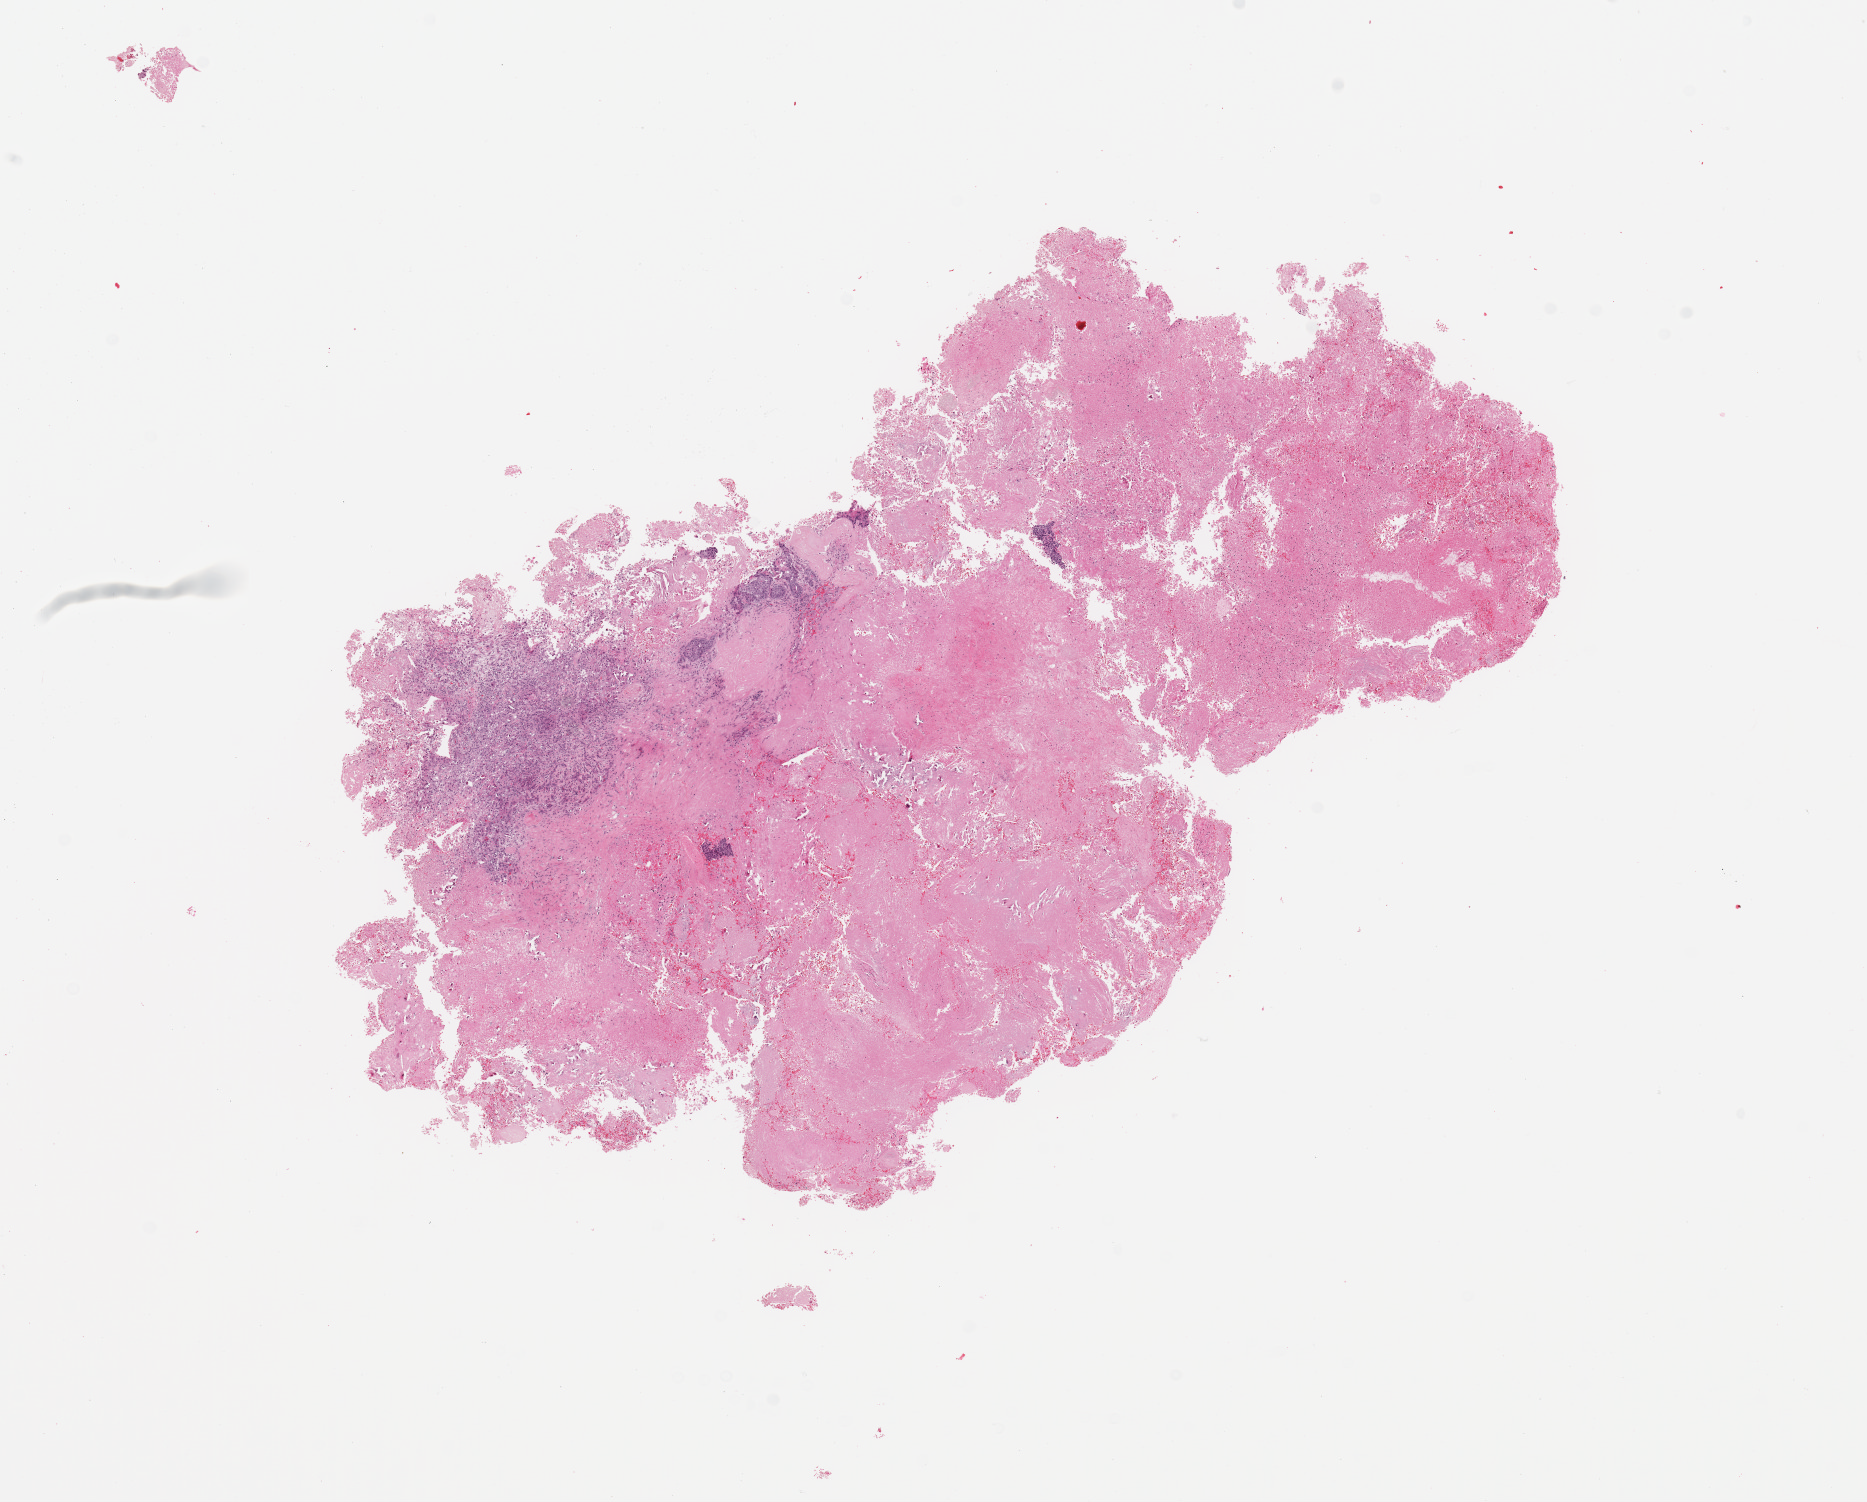
Hematoxylin and eosin (H&E) stained whole-slide image, shown as a low-resolution overview of the whole scanned area (about 14.8 x 11.9 mm); lung, tumour tissue. 78-year-old male patient. Histologic grade: G2 (moderately differentiated).
Histologic diagnosis: Squamous cell carcinoma, NOS. Primary tumour site (as recorded): right middle lobe. AJCC pathologic stage: III.